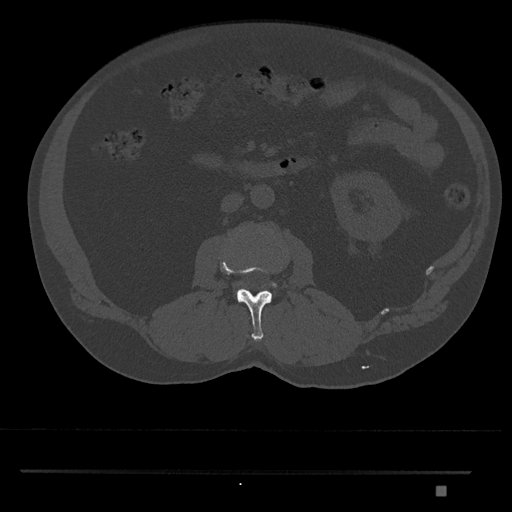
CT including the spine, one axial slice. Position 729 of 1134 along the scan axis. Reconstruction kernel Br40s/3. Bone window (W 1800 / L 400 HU). 512 × 512 image matrix. Male patient, age 65 years. Case-level facts recorded for this patient, not image findings: primary cancer: prostate.
Structures marked on this image (semi-automatic segmentation, software-assisted and operator-edited):
- L2 vertebra: box from (x=219, y=257) to (x=272, y=342) px
- L3 vertebra: (x=271, y=282)–(x=276, y=287)